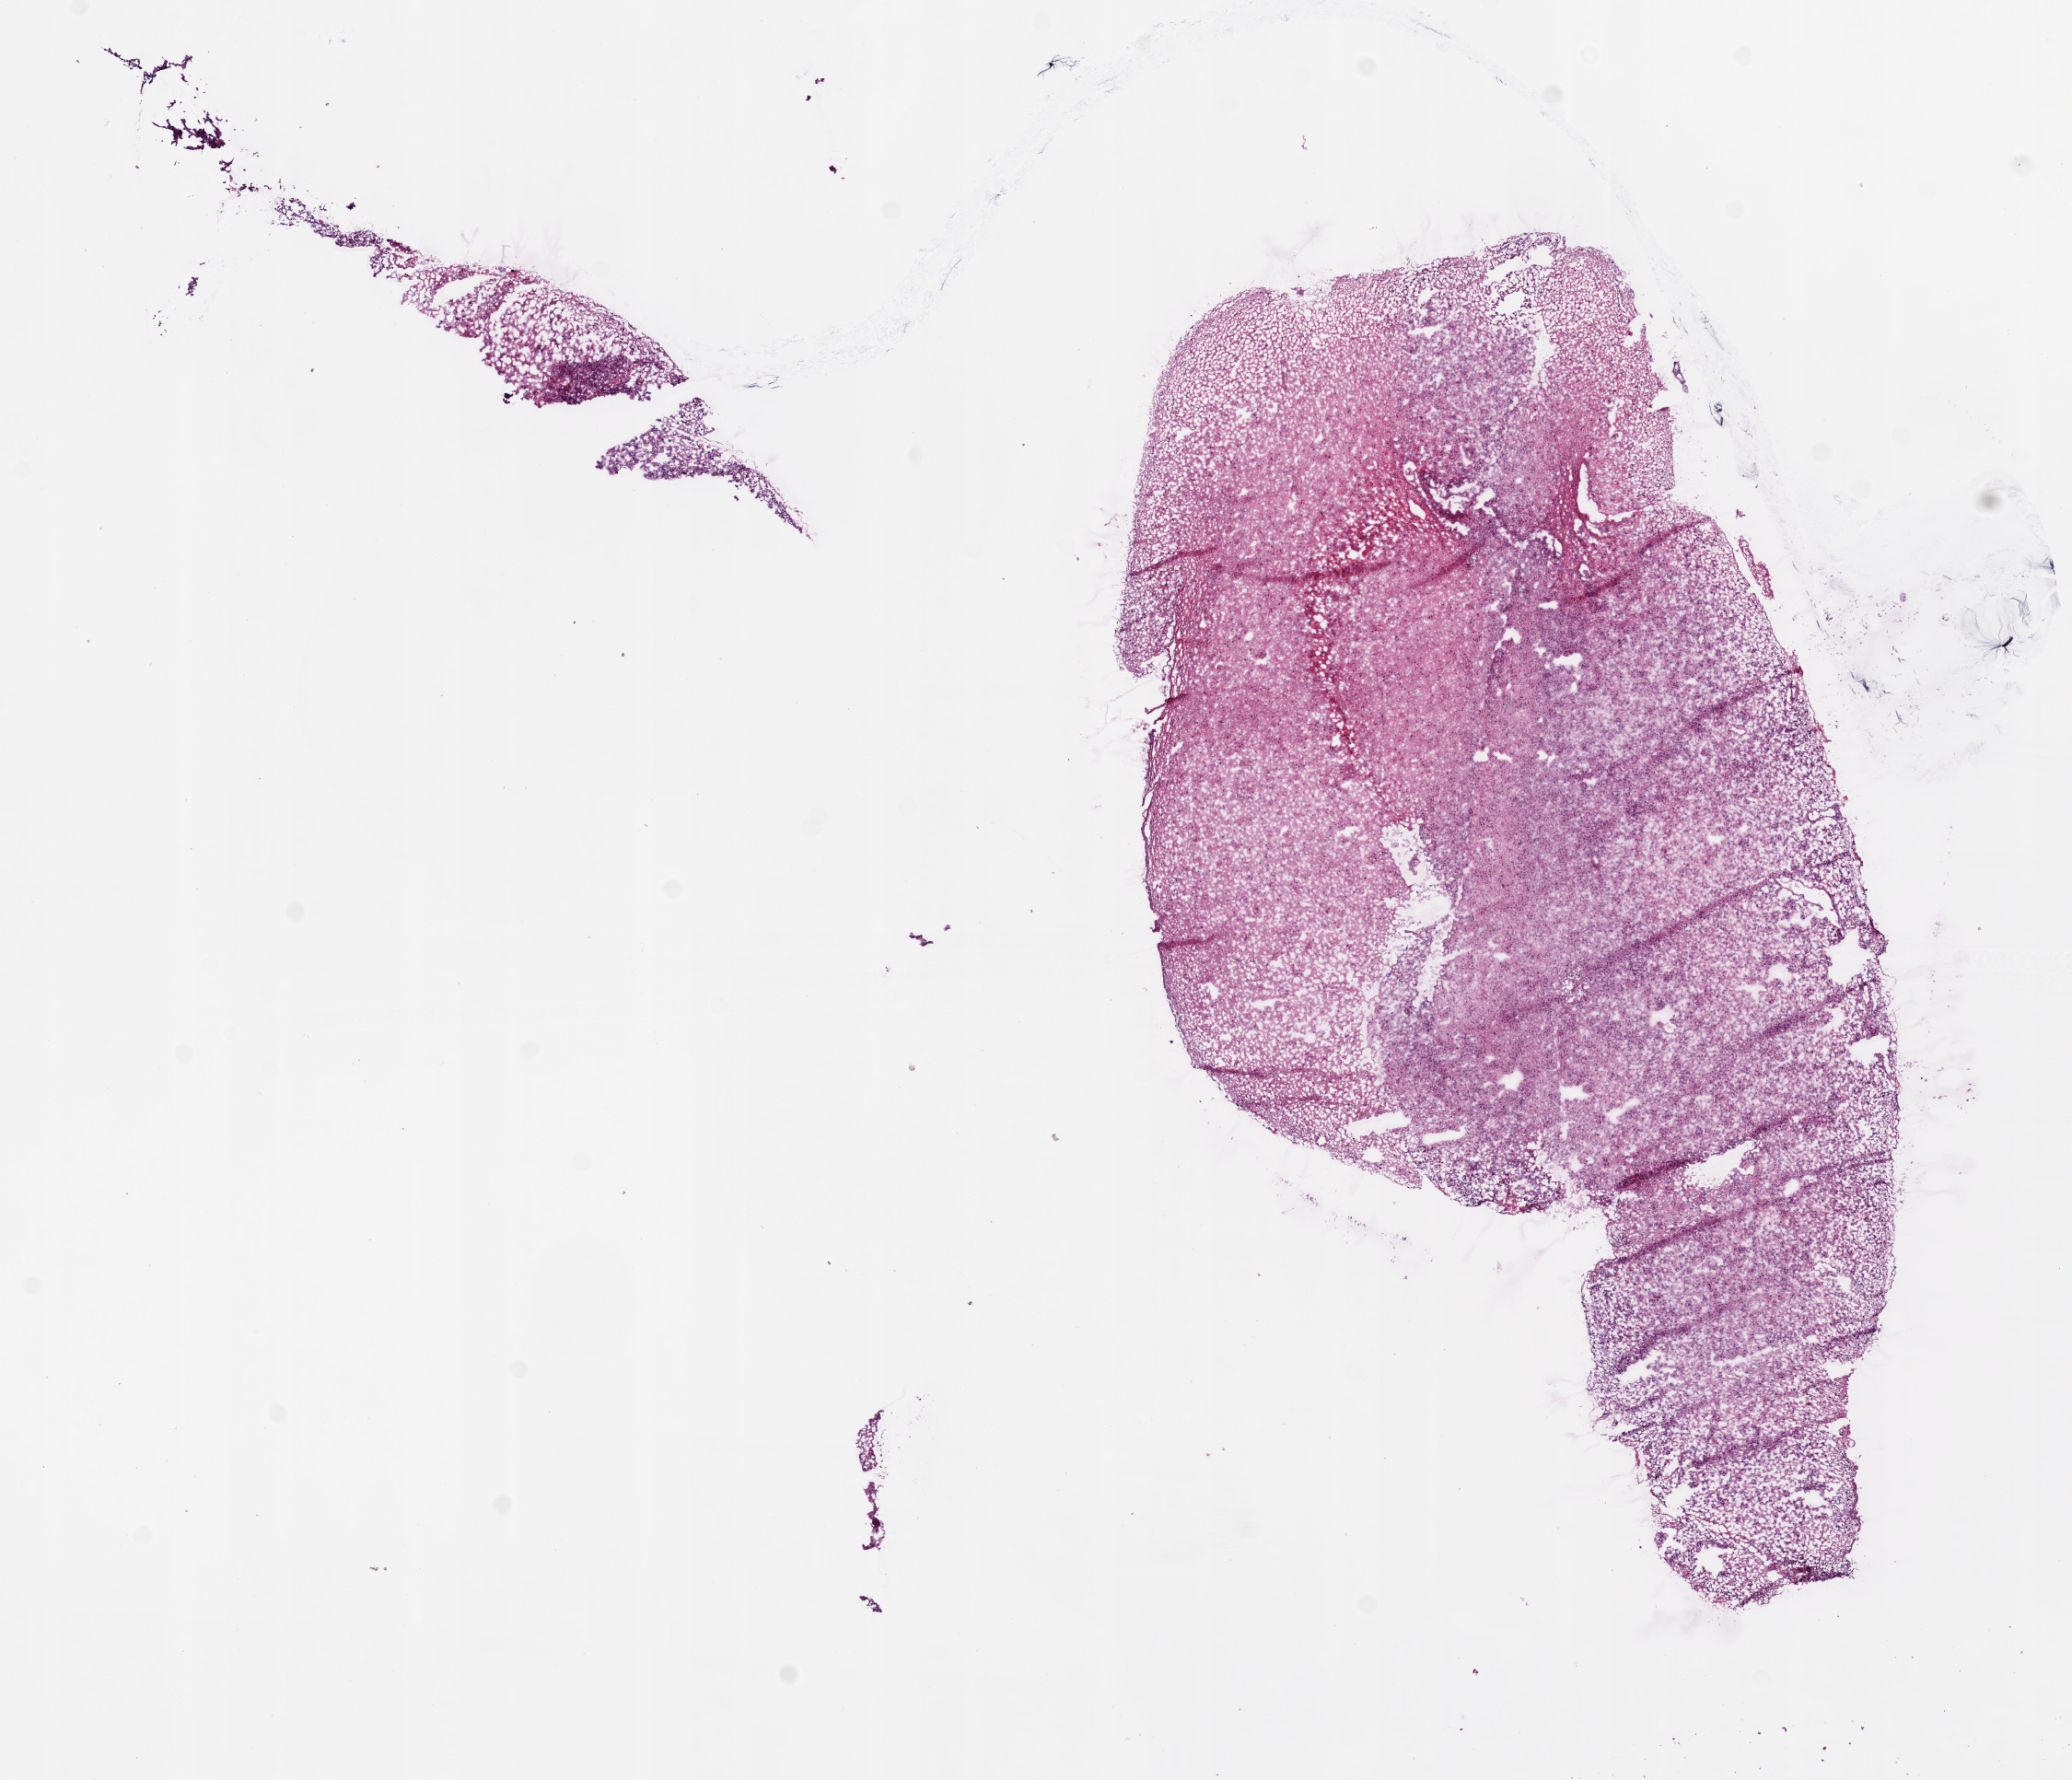
H&E whole-slide image, whole scanned area (about 9.0 x 7.8 mm) shown as a low-resolution overview, frozen section from the bottom of the tissue portion, brain, primary tumour sample. Male, age 34 years at initial diagnosis. Slide review estimates, as recorded: tumour cells 100%, tumour nuclei 85%, normal cells 0%, stromal cells 0%, necrosis 0%.
- histologic diagnosis: Glioblastoma